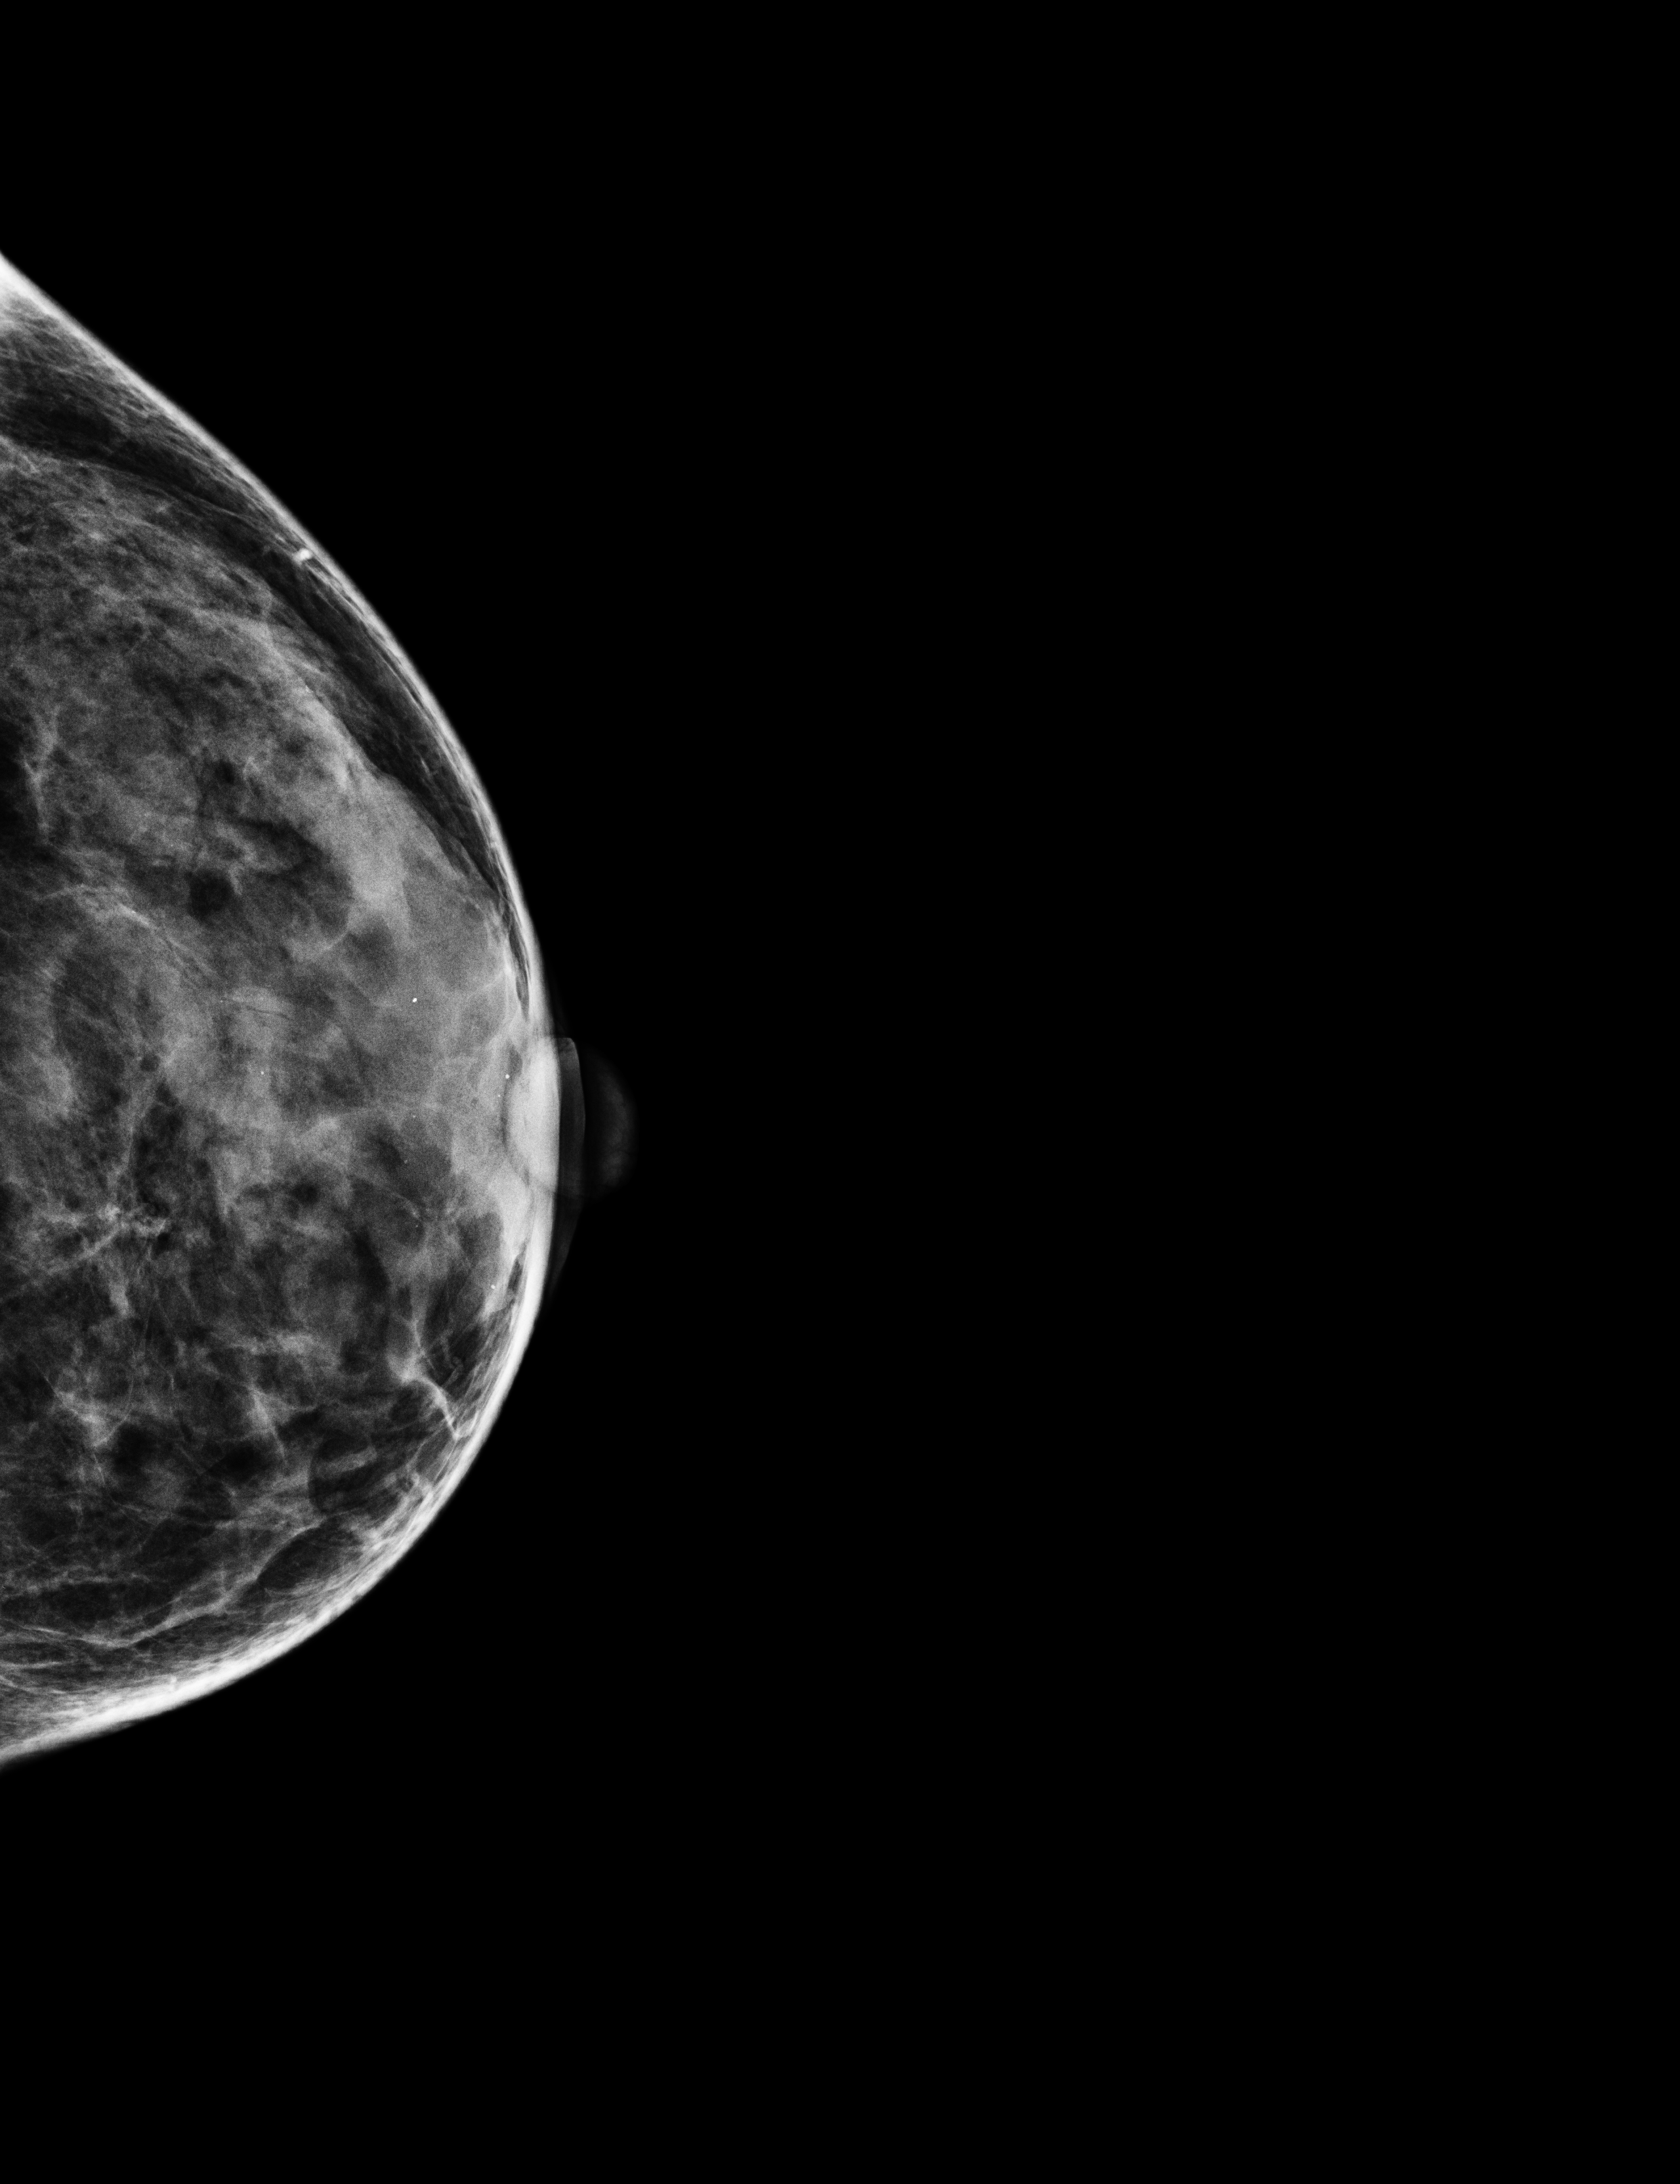
Full-field digital mammogram (FFDM); left breast; CC view; screening examination. Female patient, age 56 years.
Breast density at the screening exam (both breasts): heterogeneously dense (BI-RADS density category c). Final BI-RADS assessment for this screening round (tomosynthesis exam, both breasts): category 2. Recall: recalled for additional imaging after this screen.